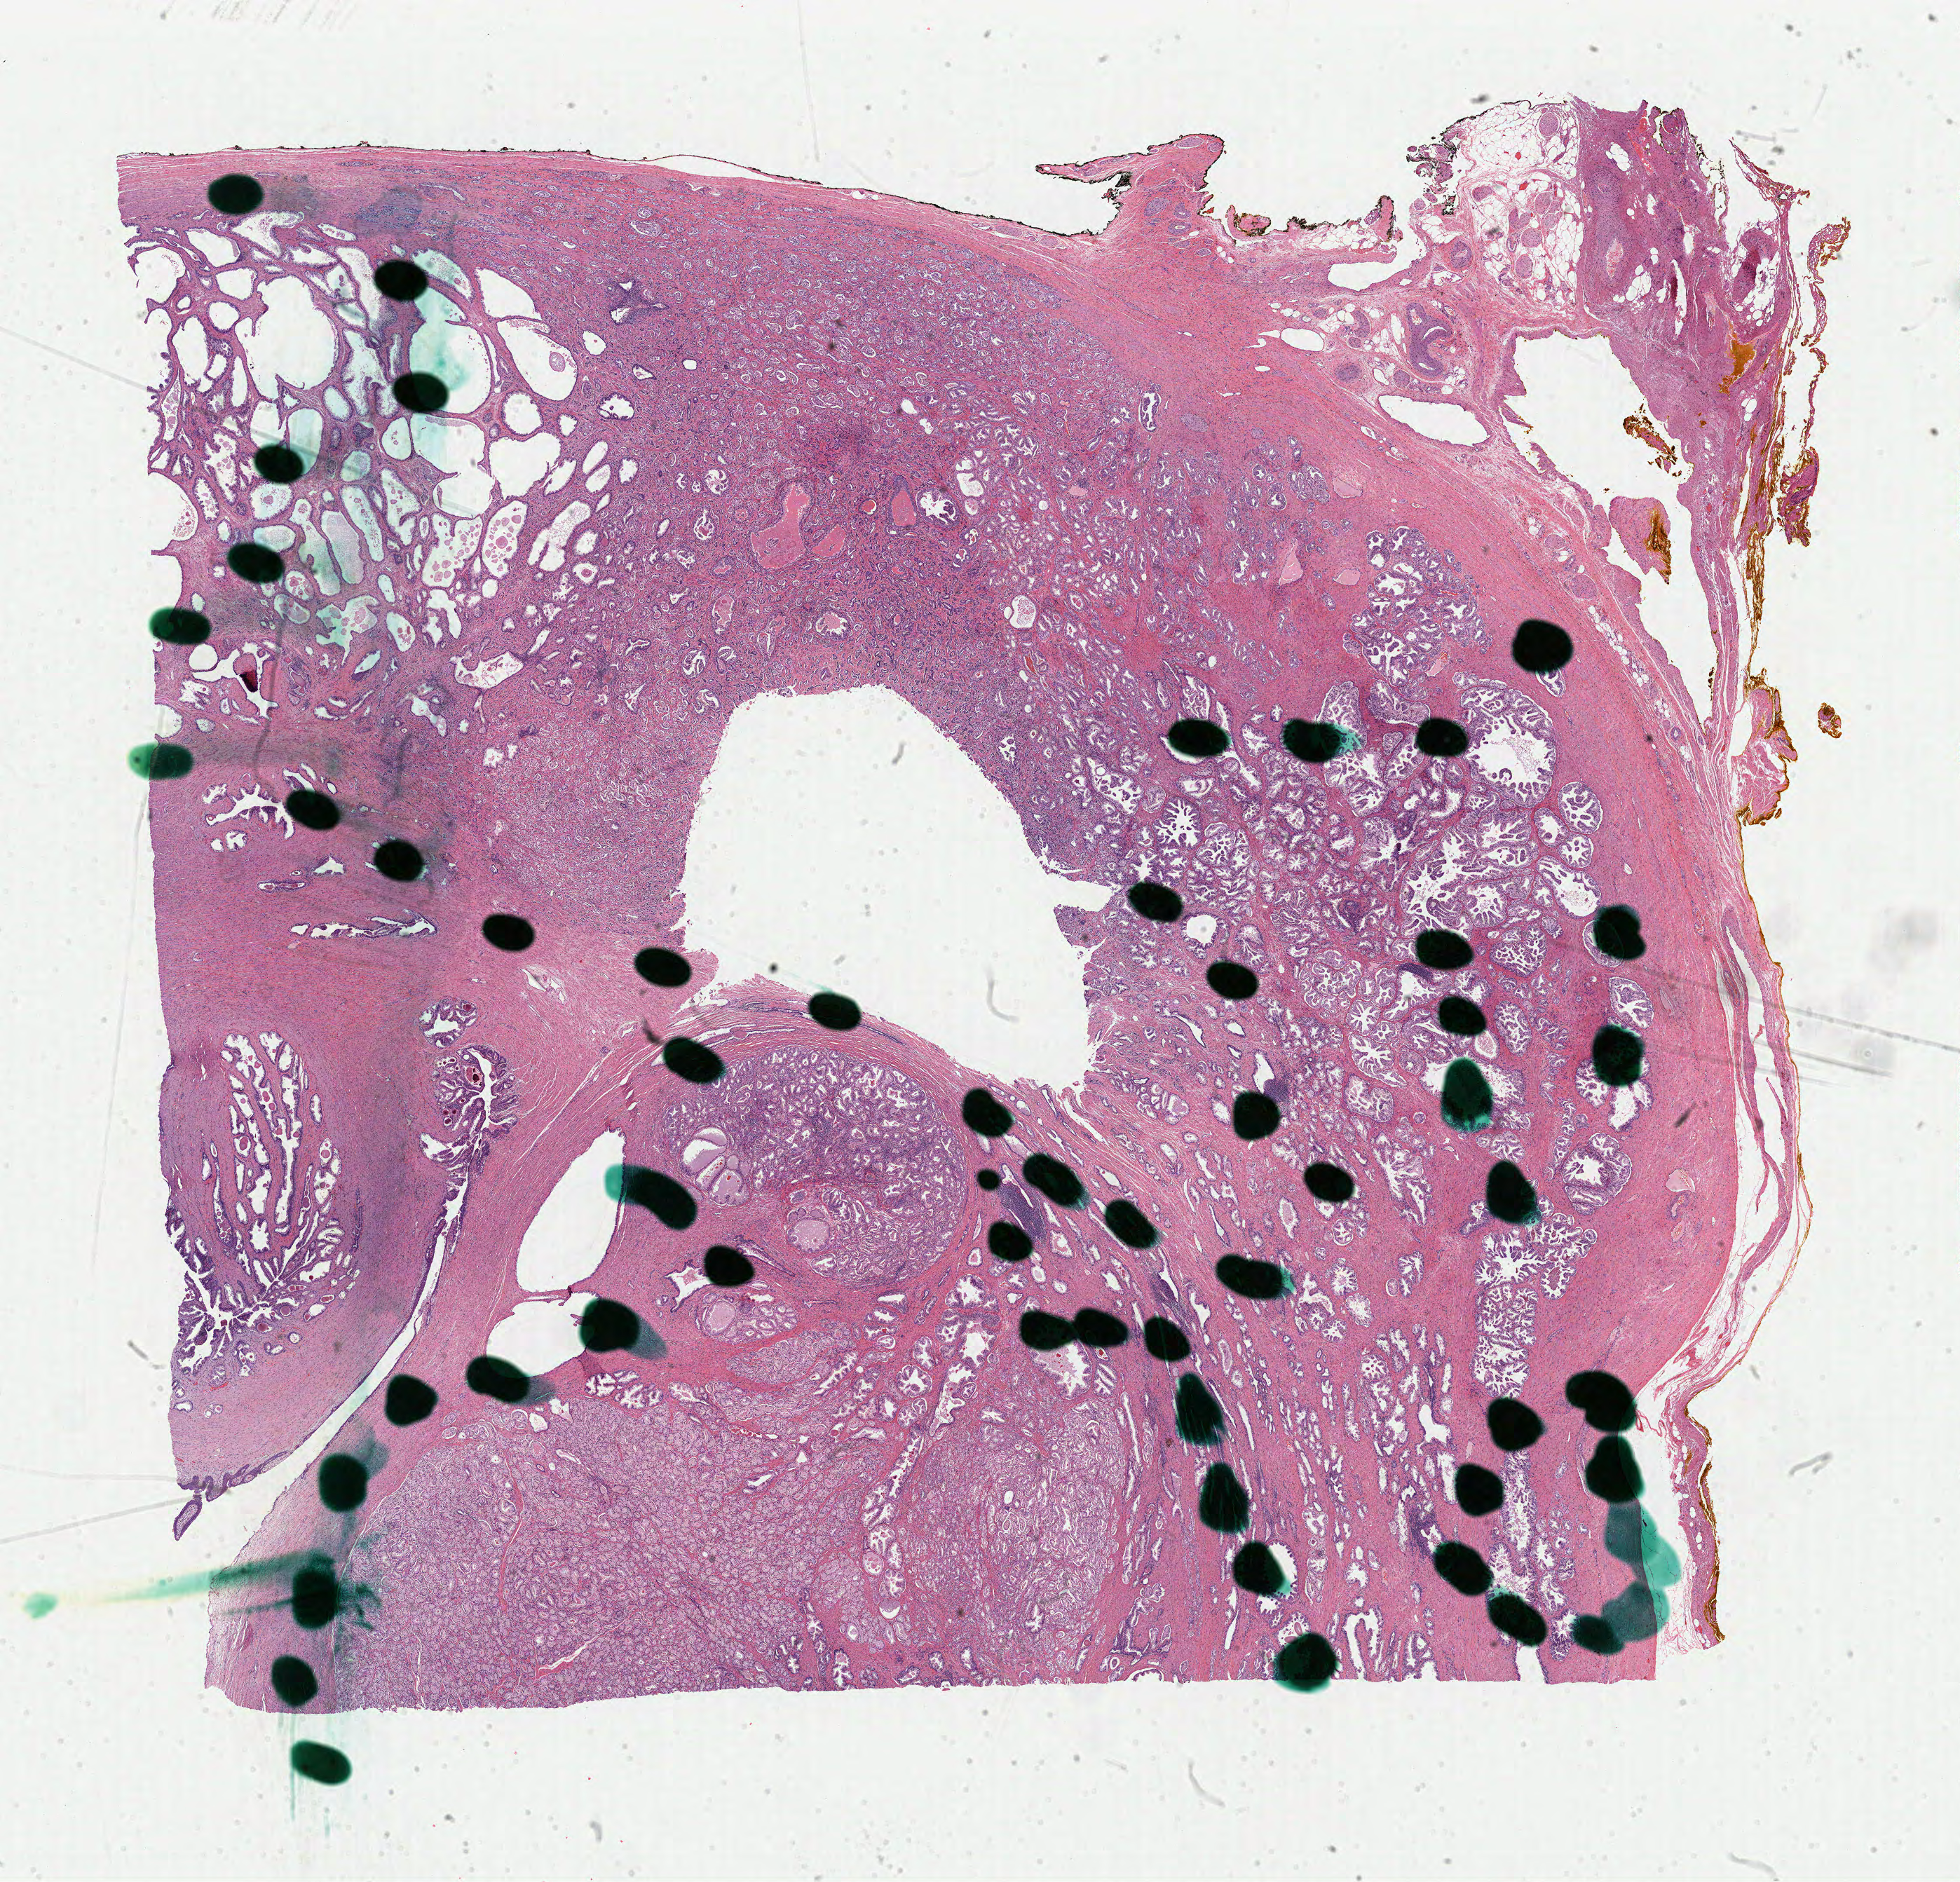
Whole-slide histology image, Hematoxylin and eosin (H&E) stained, low-resolution overview of the scanned area, about 22.1 x 21.2 mm (acquisition: 40x scan), formalin-fixed paraffin-embedded (FFPE) diagnostic section, primary tumour sample from the prostate. Patient: male, age at initial diagnosis 63 years.
Diagnosis: Adenocarcinoma, NOS (prostate gland).